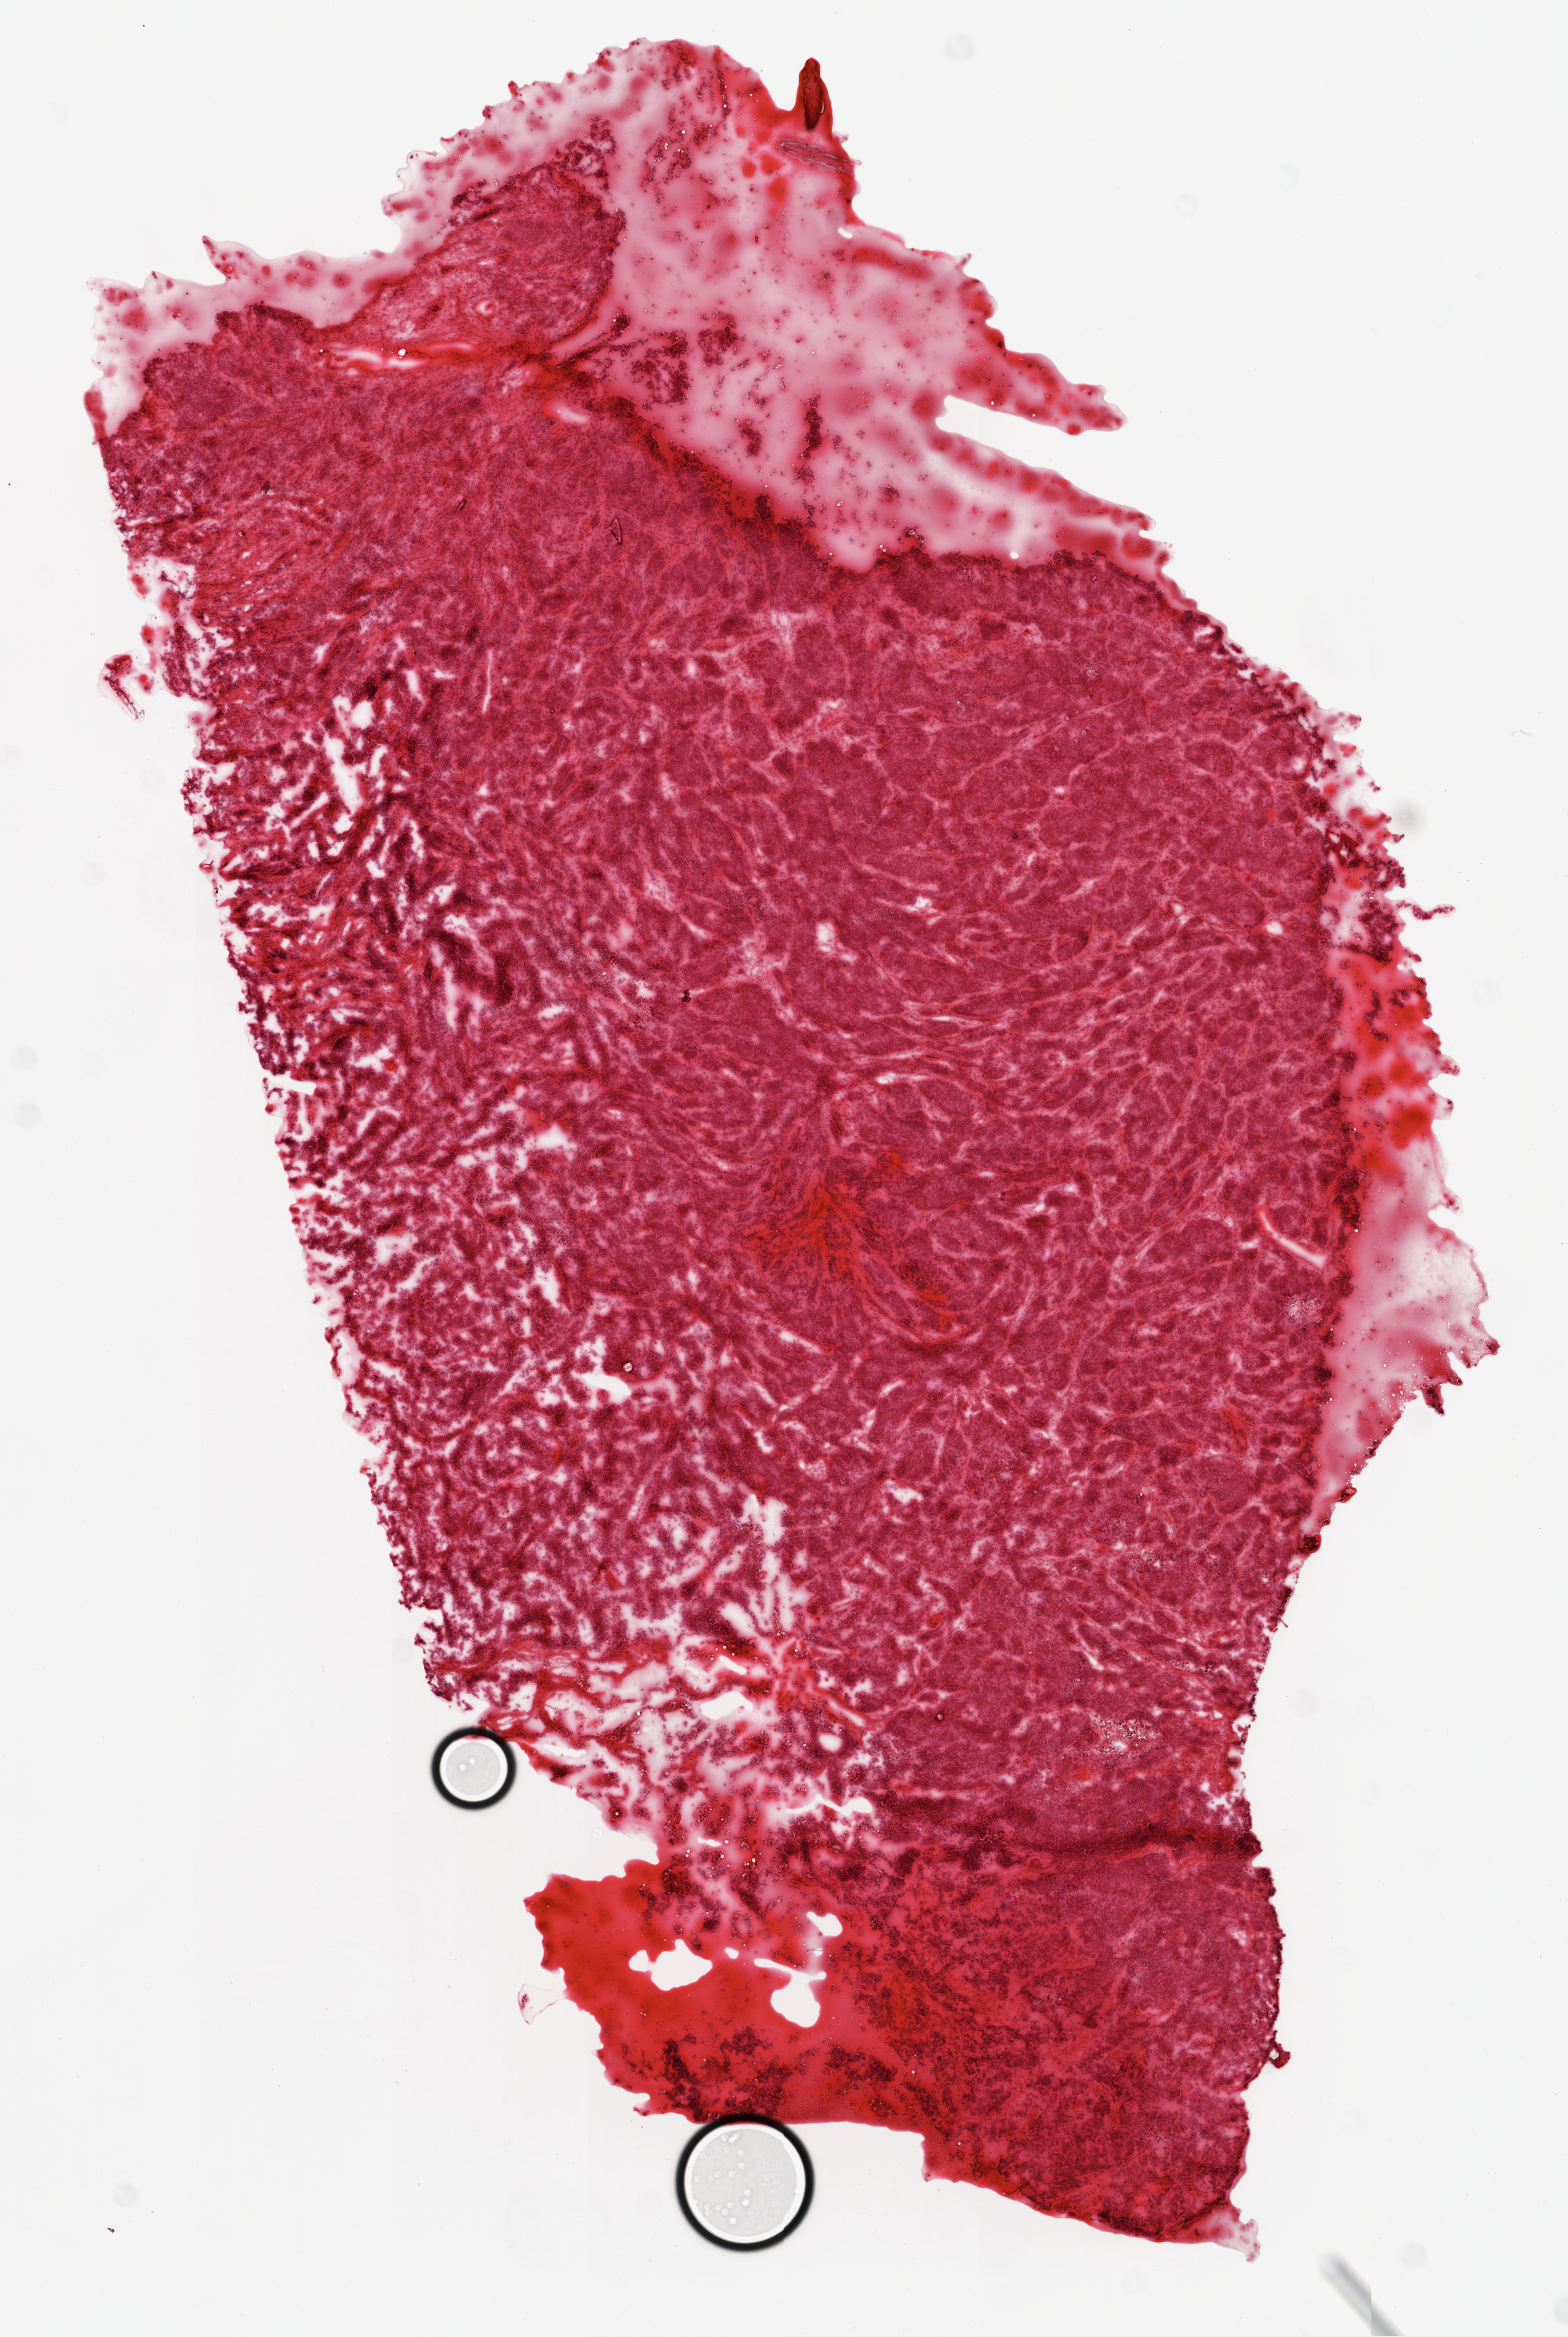
H&E whole-slide image, low-resolution overview of the scanned area, about 8.0 x 12.0 mm (from a 20x scan). Frozen section from the top of the tissue portion. Primary tumour sample from the ovary. Female, age 57 years at initial diagnosis. Pathologist review of this section (percent, as recorded): tumour cells 95%, tumour nuclei 99%.
Pathologic diagnosis: Serous cystadenocarcinoma, NOS.